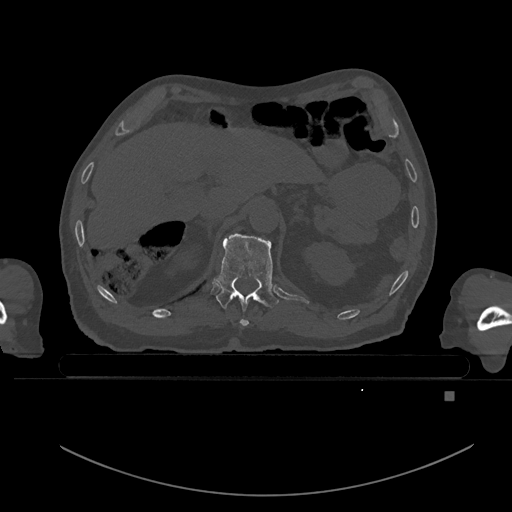
CT including the spine, one axial slice. Position 33 of 969 along the scan axis. Bone window (W 1800 / L 400 HU). 0.5 mm slice thickness. 512 × 512 image matrix. Patient: male, 82 years. From the clinical record (not read from this slice): primary cancer: prostate; vertebrae with lytic lesions (as recorded): T11, T9, T8, T2.
Annotated regions visible in this slice (semi-automatic segmentation, software-assisted and operator-edited):
- T11 vertebra: bounding box <214,233,279,326> (left, top, right, bottom; pixels)